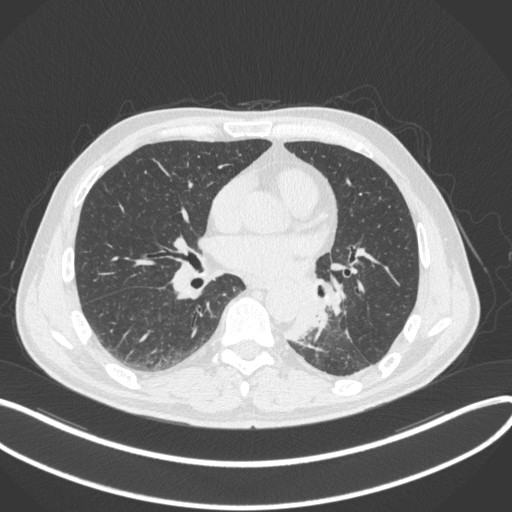
Chest CT, one axial slice; position 156 of 328 along the scan axis; reconstruction kernel B31f; lung window (W 1500 / L -600 HU); 512 × 512 image matrix. Male patient, age 59 years. From the clinical record (not read from this slice): clinical TNM (as recorded): T2a N2 M0.
Structures marked on this image (bounding box drawn by a radiologist):
- lung tumour (recorded histology: squamous cell carcinoma): bounding box (x1, y1, x2, y2) in pixels: (285, 284, 334, 349)